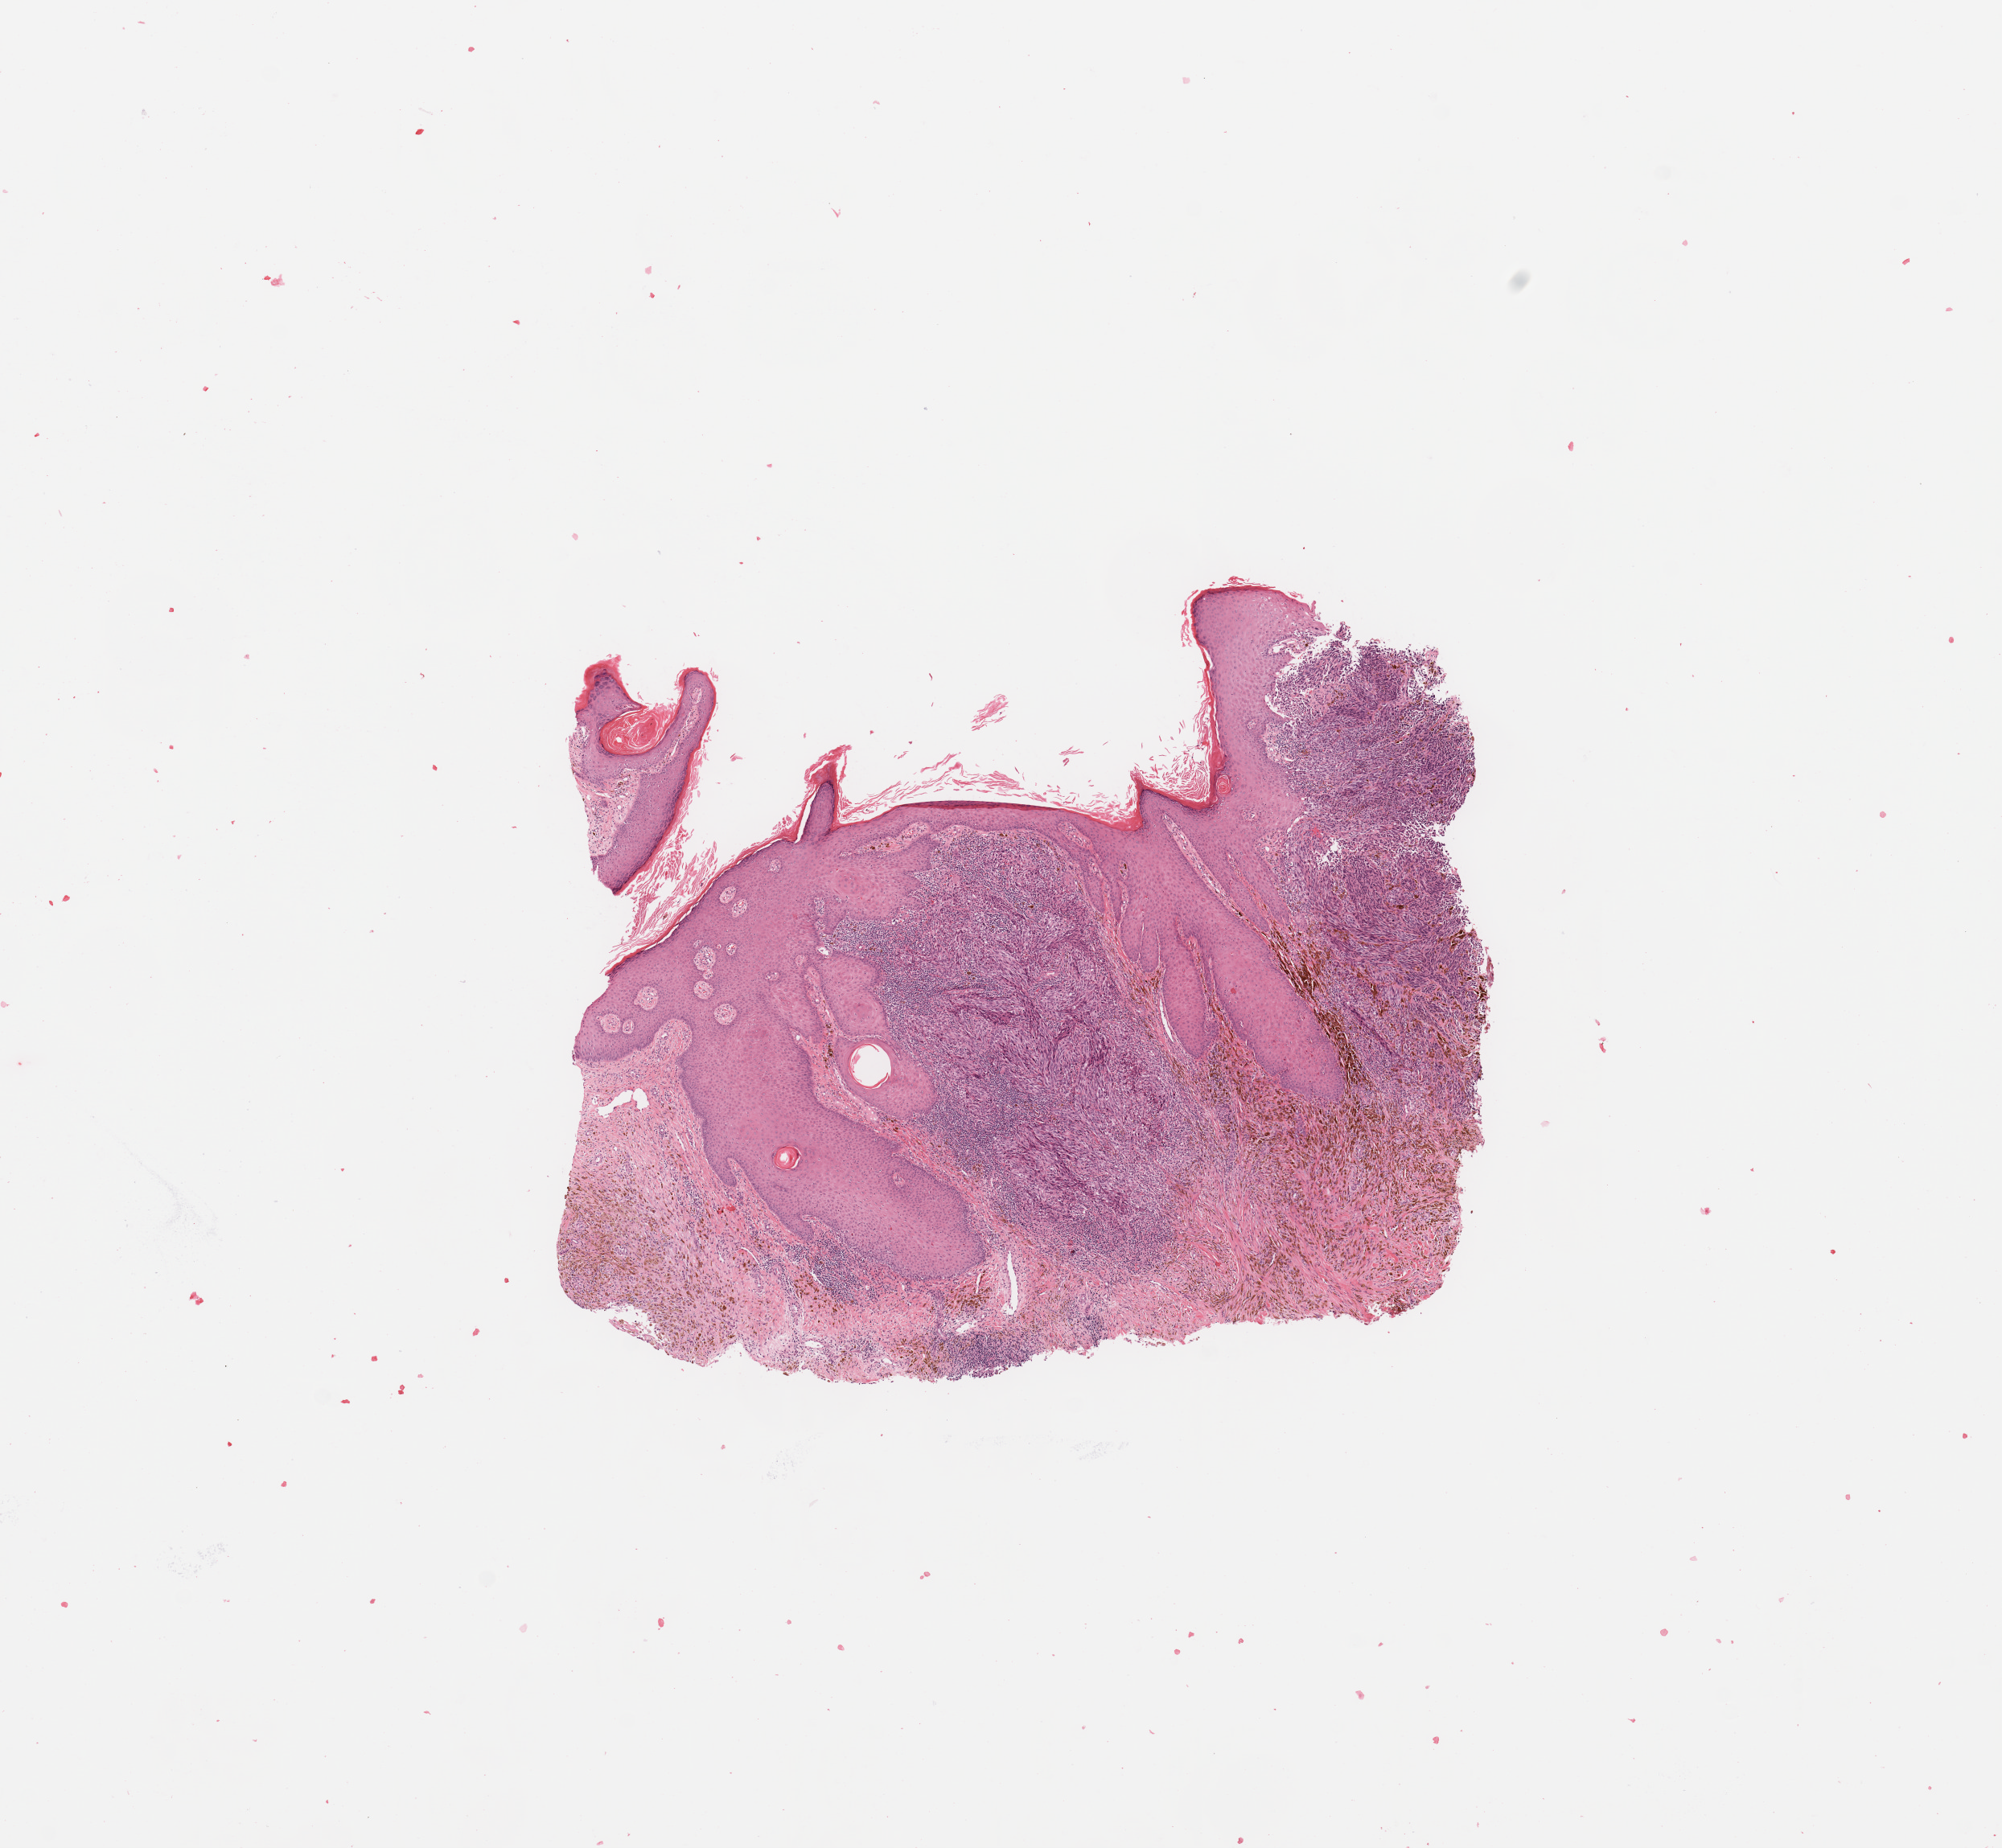
Digitized H&E-stained tissue section (whole slide) — shown as a low-resolution overview of the whole scanned area (about 9.8 x 9.1 mm), melanoma tumour tissue; sampled site not recorded. Female, 45 y/o.
Patient diagnosis (cohort enrolment): cutaneous melanoma (skin).